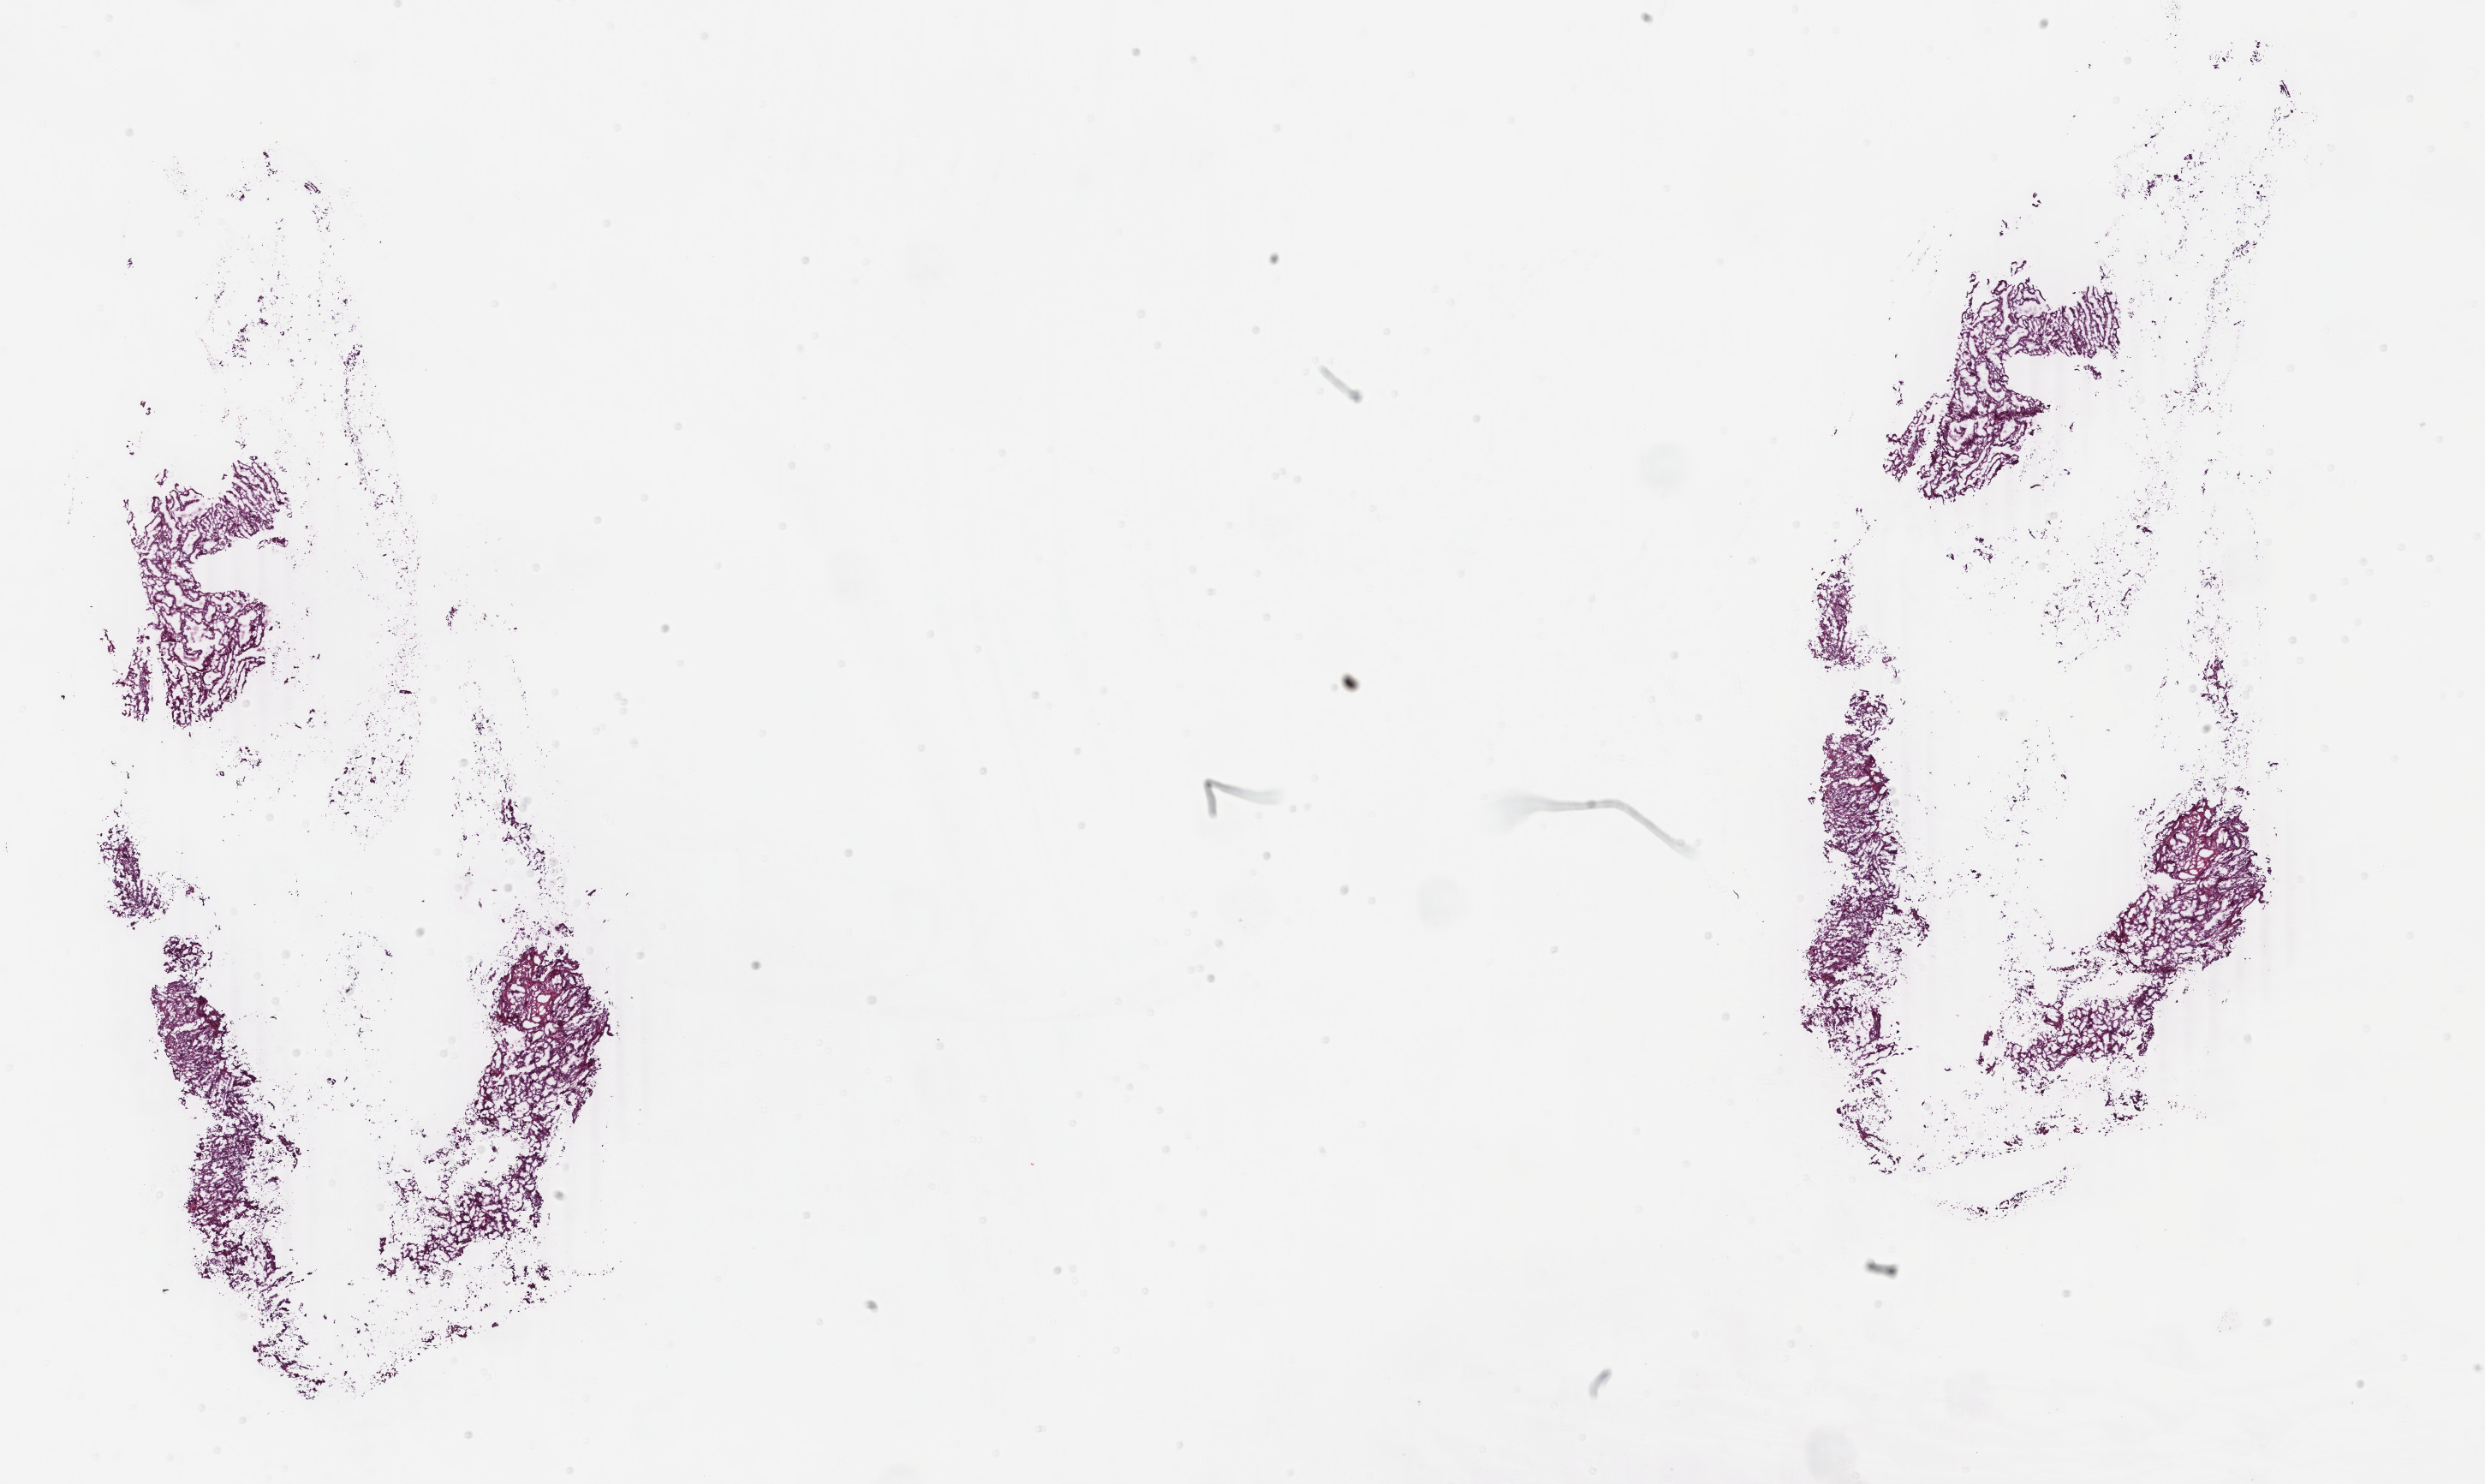
Whole-slide histology image, H&E — shown as a low-resolution overview of the whole scanned area (about 23.1 x 13.8 mm). Frozen section. Sample: primary tumour, uterus. Patient: female, age at initial diagnosis 63 years.
Pathologic diagnosis: Endometrioid adenocarcinoma, NOS.